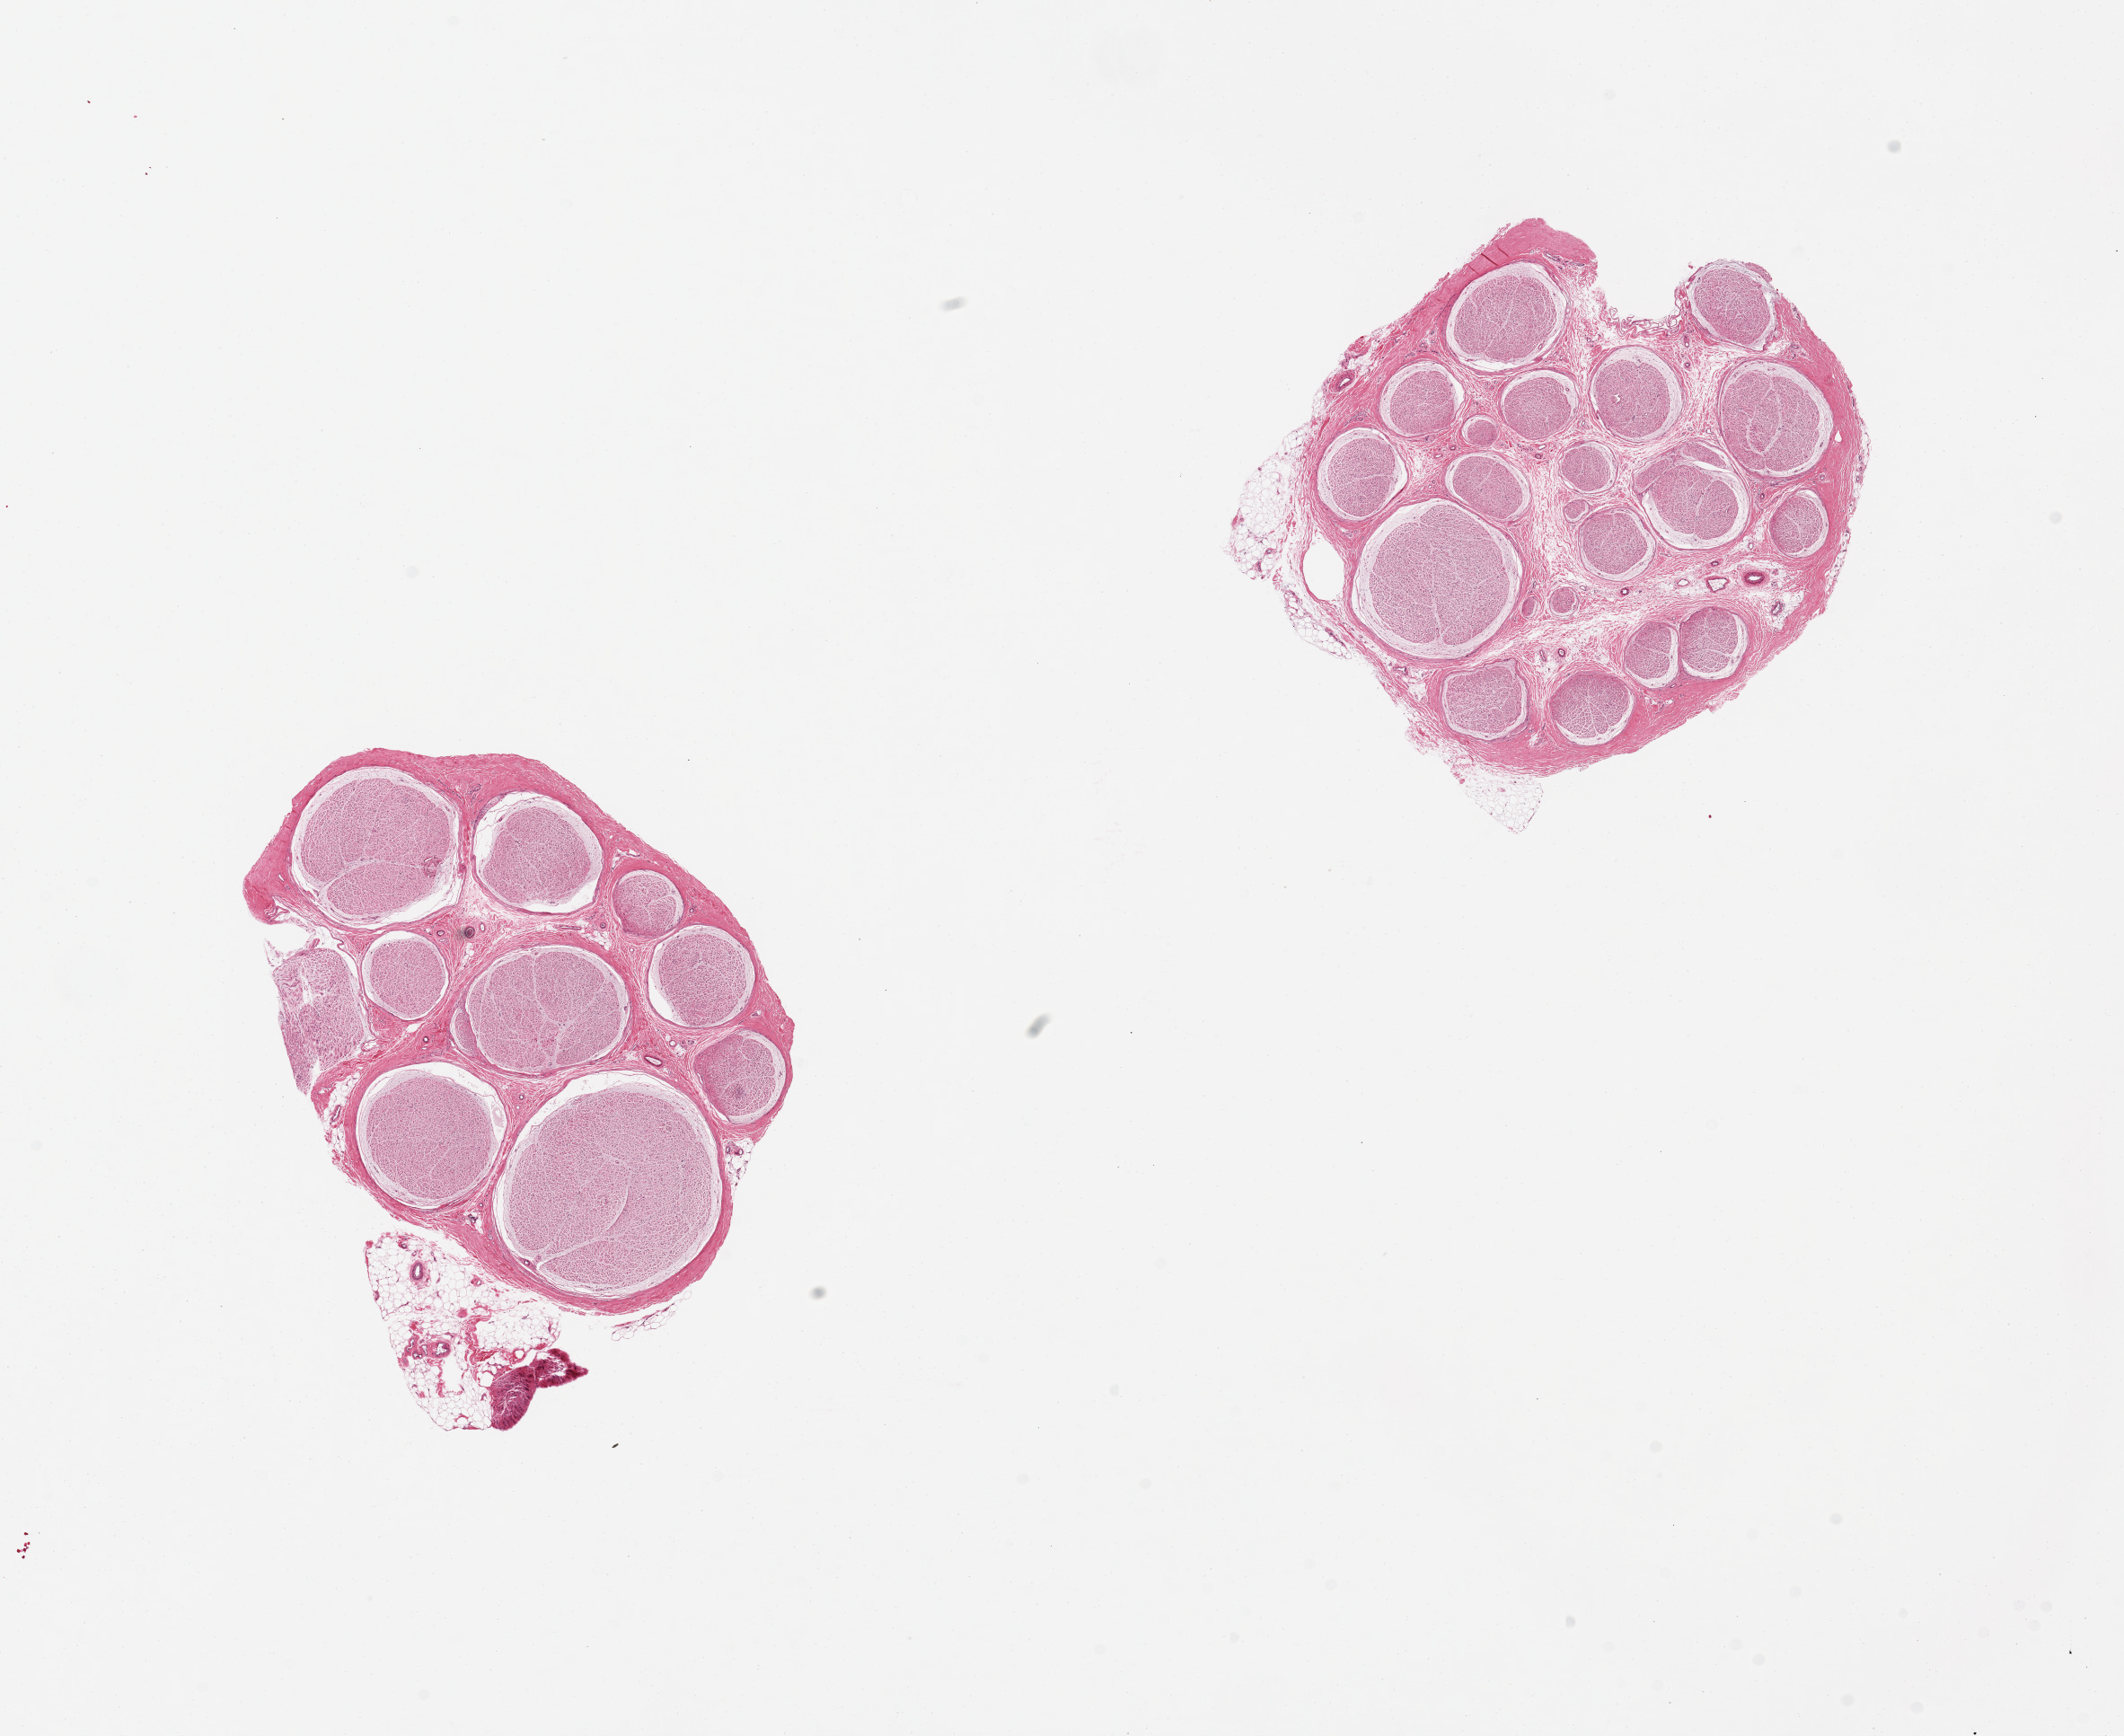
Haematoxylin and eosin whole-slide image — shown as a low-resolution overview of the whole scanned area (about 18.7 x 15.3 mm, acquisition: 20x scan). PAXgene-fixed, paraffin-embedded tissue. Section of tibial nerve (target tissue). Tissue donor sample. Donor sex: male.
Reviewer comment on this tissue sample: 2 pieces, 5.5x5 & 5x5mm; 1.4mm adherent nubbin of fat on one section.